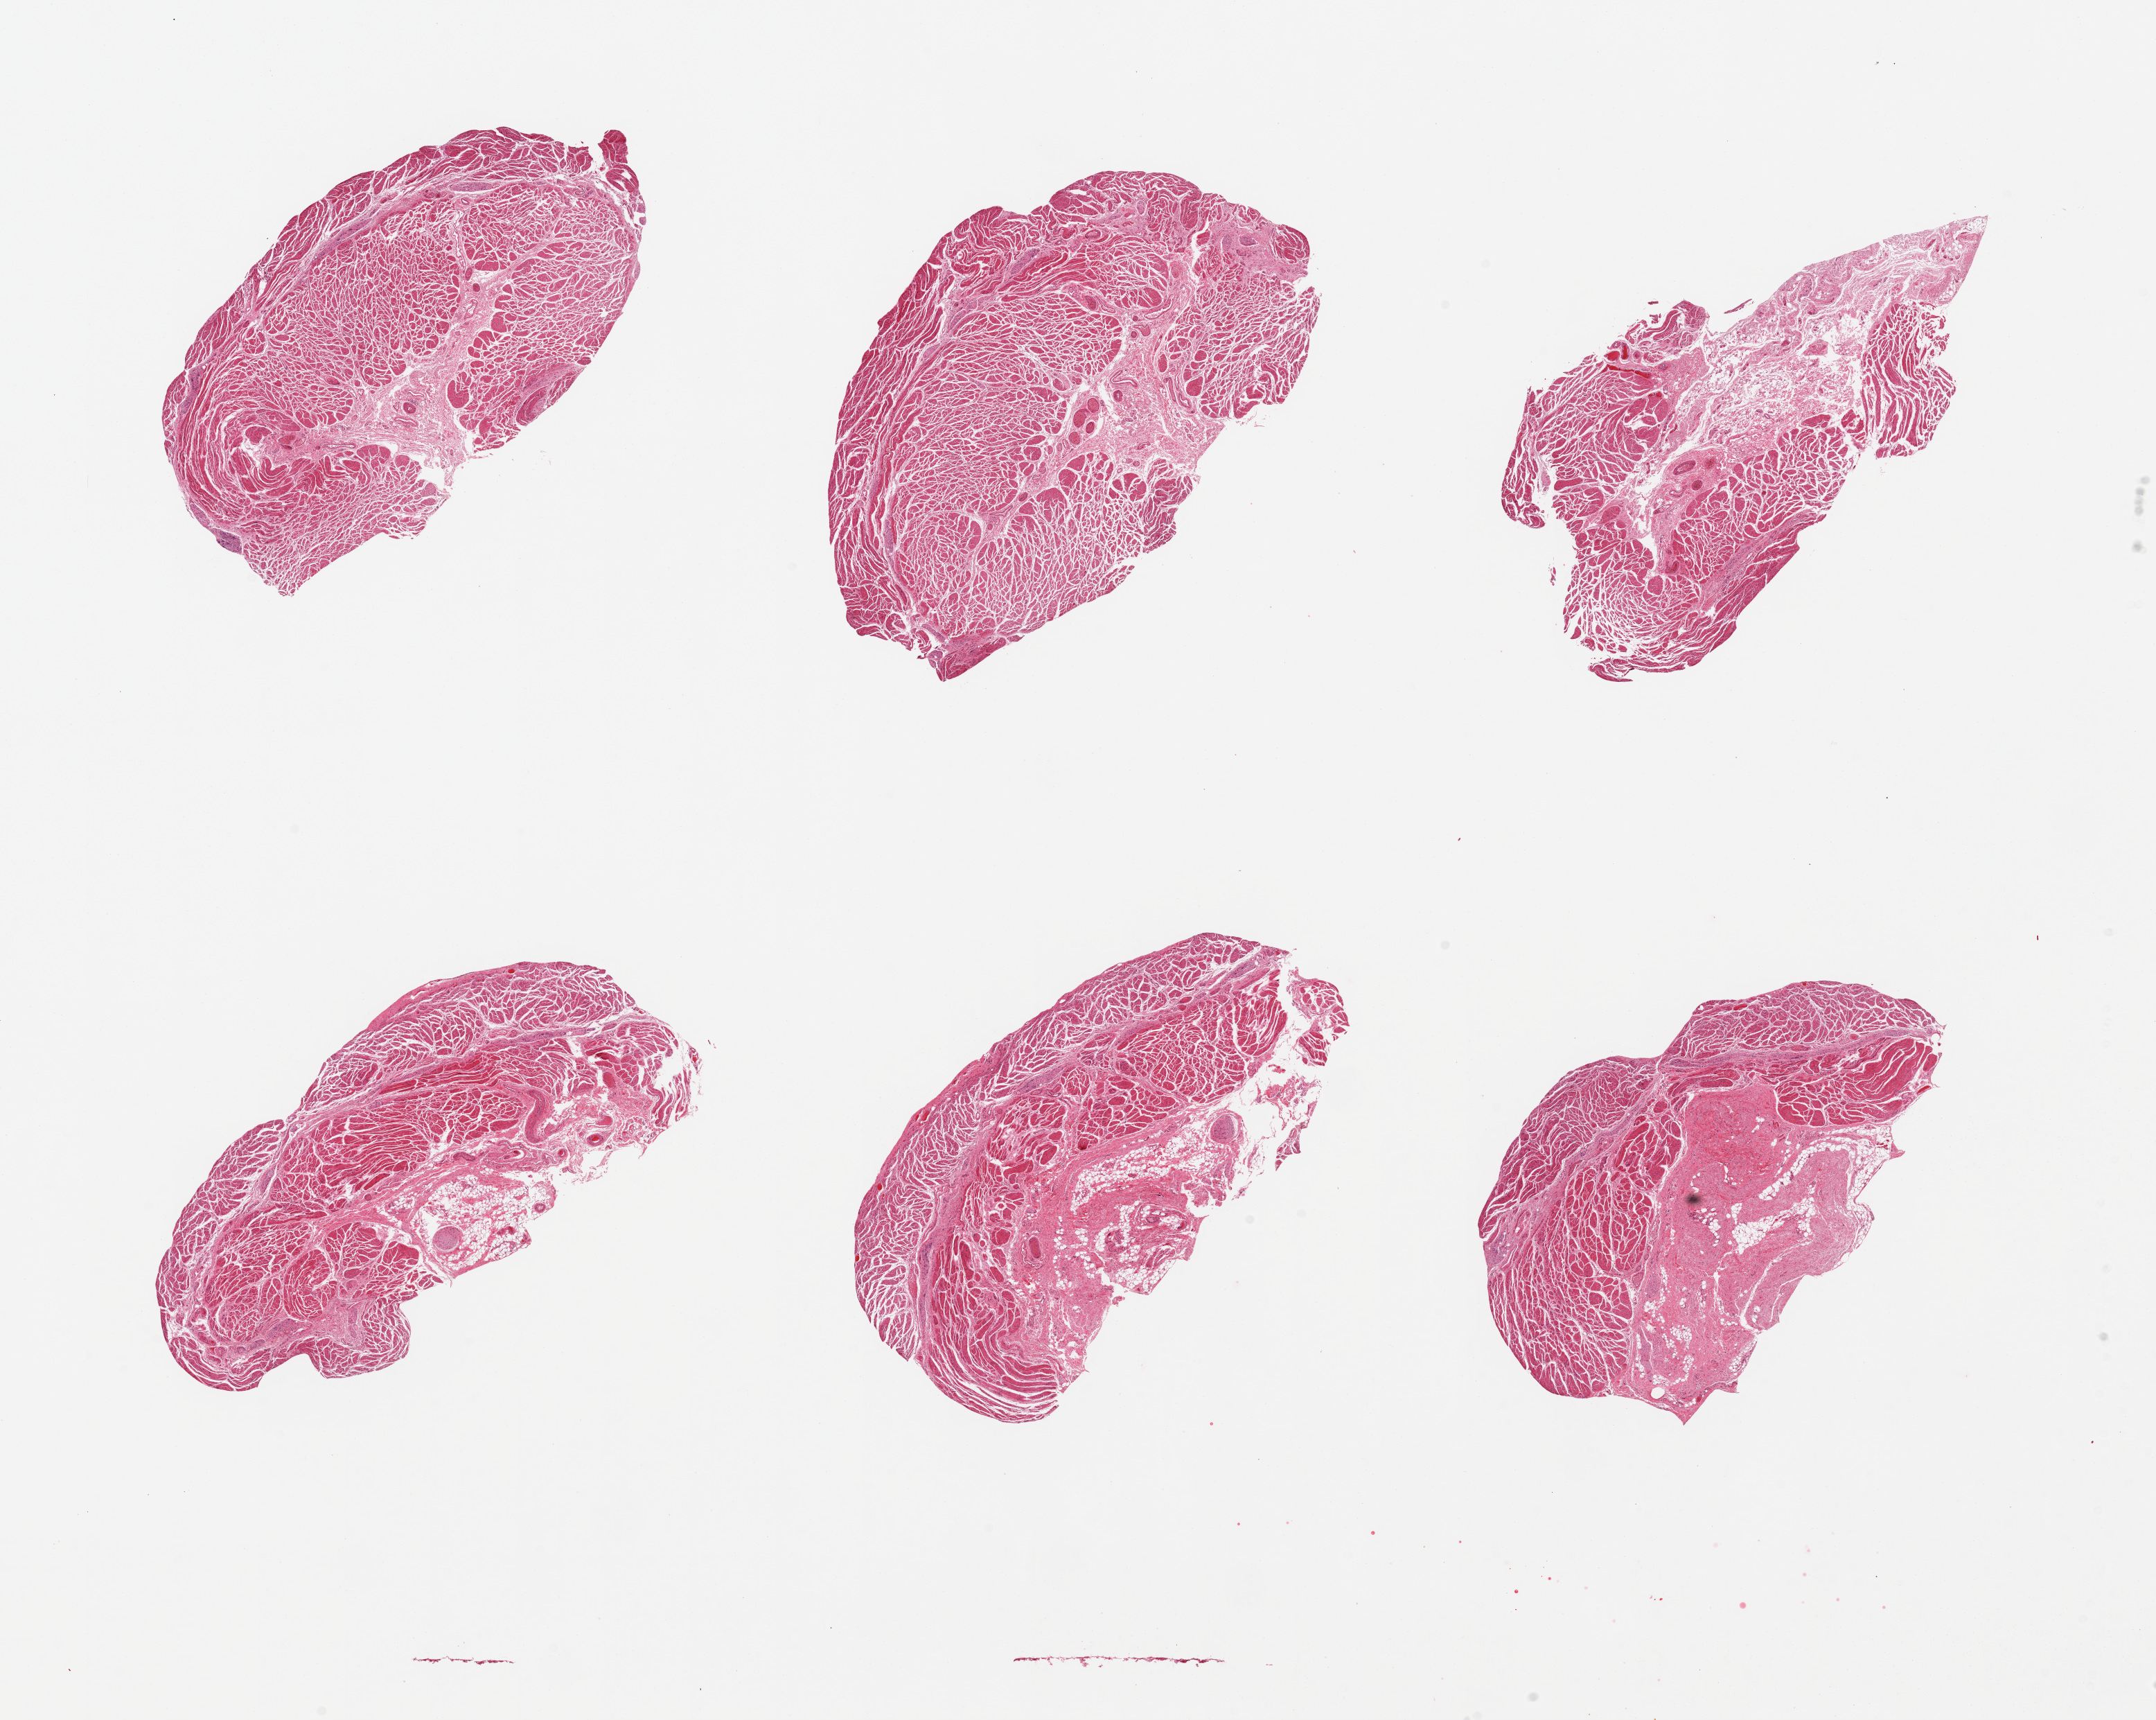
Digitized haematoxylin and eosin-stained section — low-resolution overview of the scanned area, about 24.6 x 19.6 mm (from a 20x scan); PAXgene-fixed, paraffin-embedded tissue; section of gastroesophageal junction (target tissue); tissue donor sample. Donor: male.
Pathologist's review note for this sample: 6 pieces; attached small amount of external fat and fibrovascuar tissue and nerves.